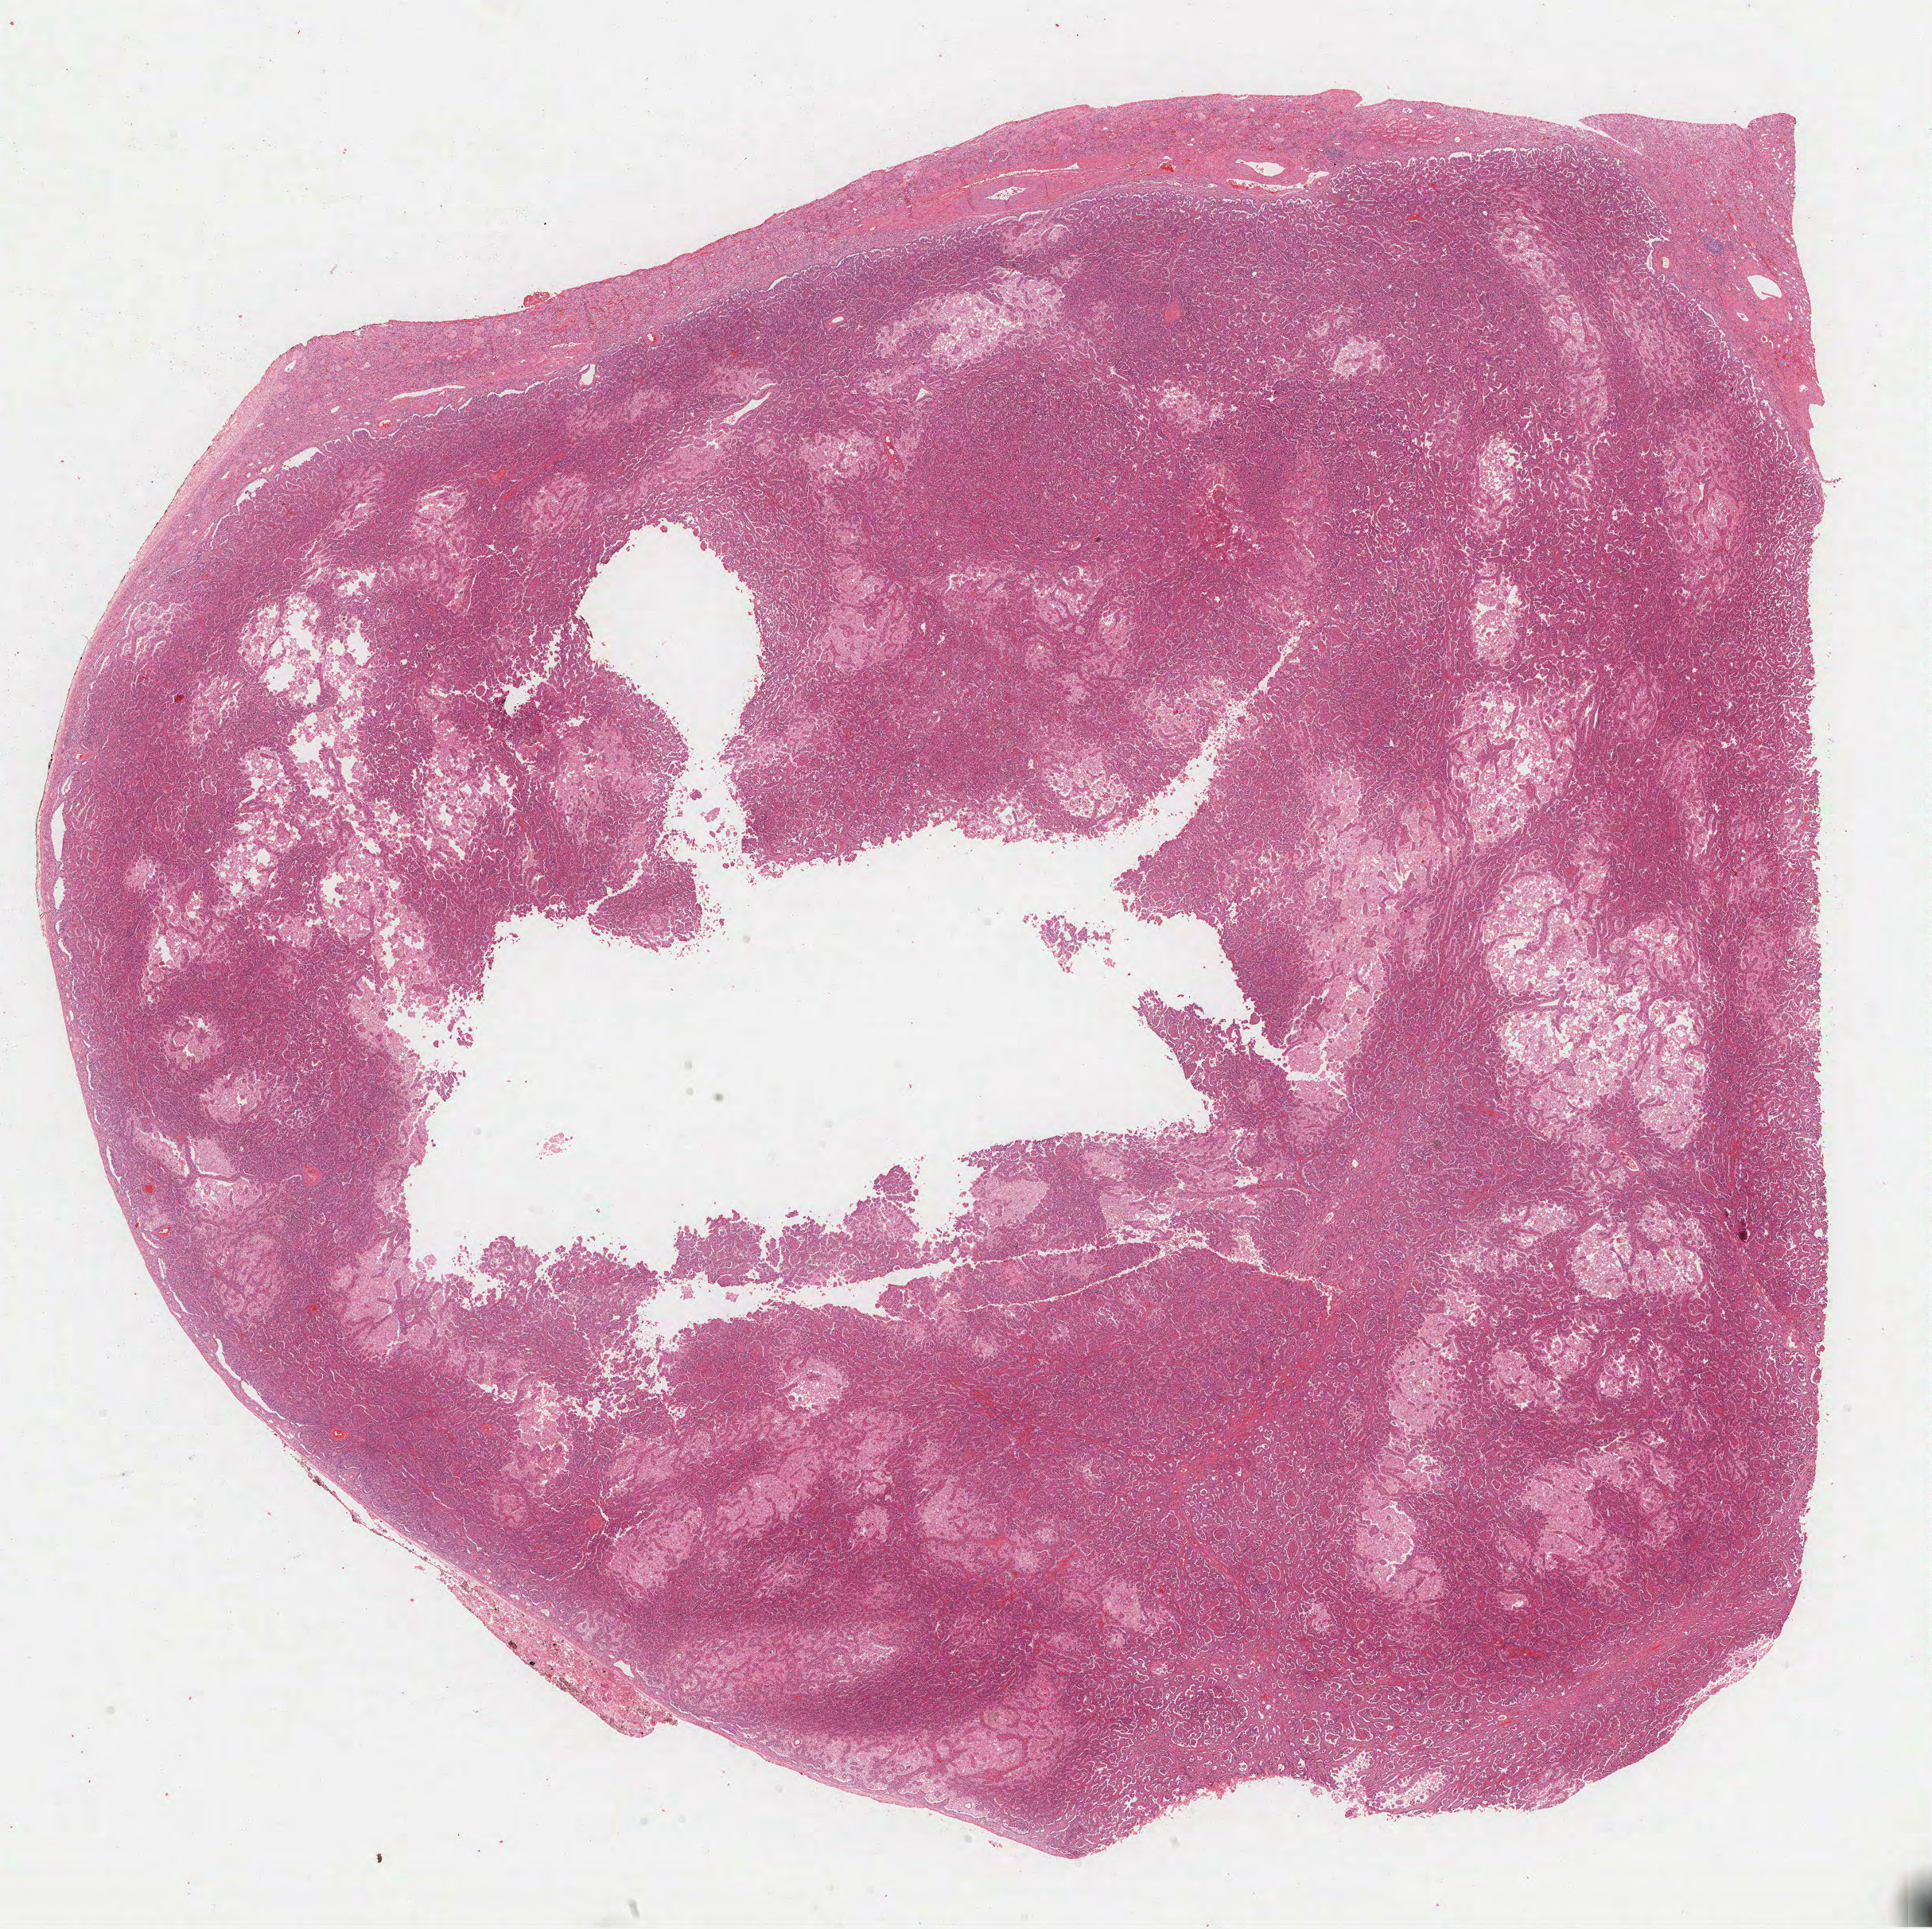
Whole-slide histology image, Hematoxylin and eosin (H&E) stained — whole scanned area (about 19.6 x 19.6 mm, from a 40x scan) shown as a low-resolution overview; formalin-fixed paraffin-embedded (FFPE) diagnostic section; sample: primary tumour, kidney. Patient: male, age at initial diagnosis 28 years.
Laterality: left. AJCC pathologic stage: I. Diagnosis: Papillary adenocarcinoma, NOS.